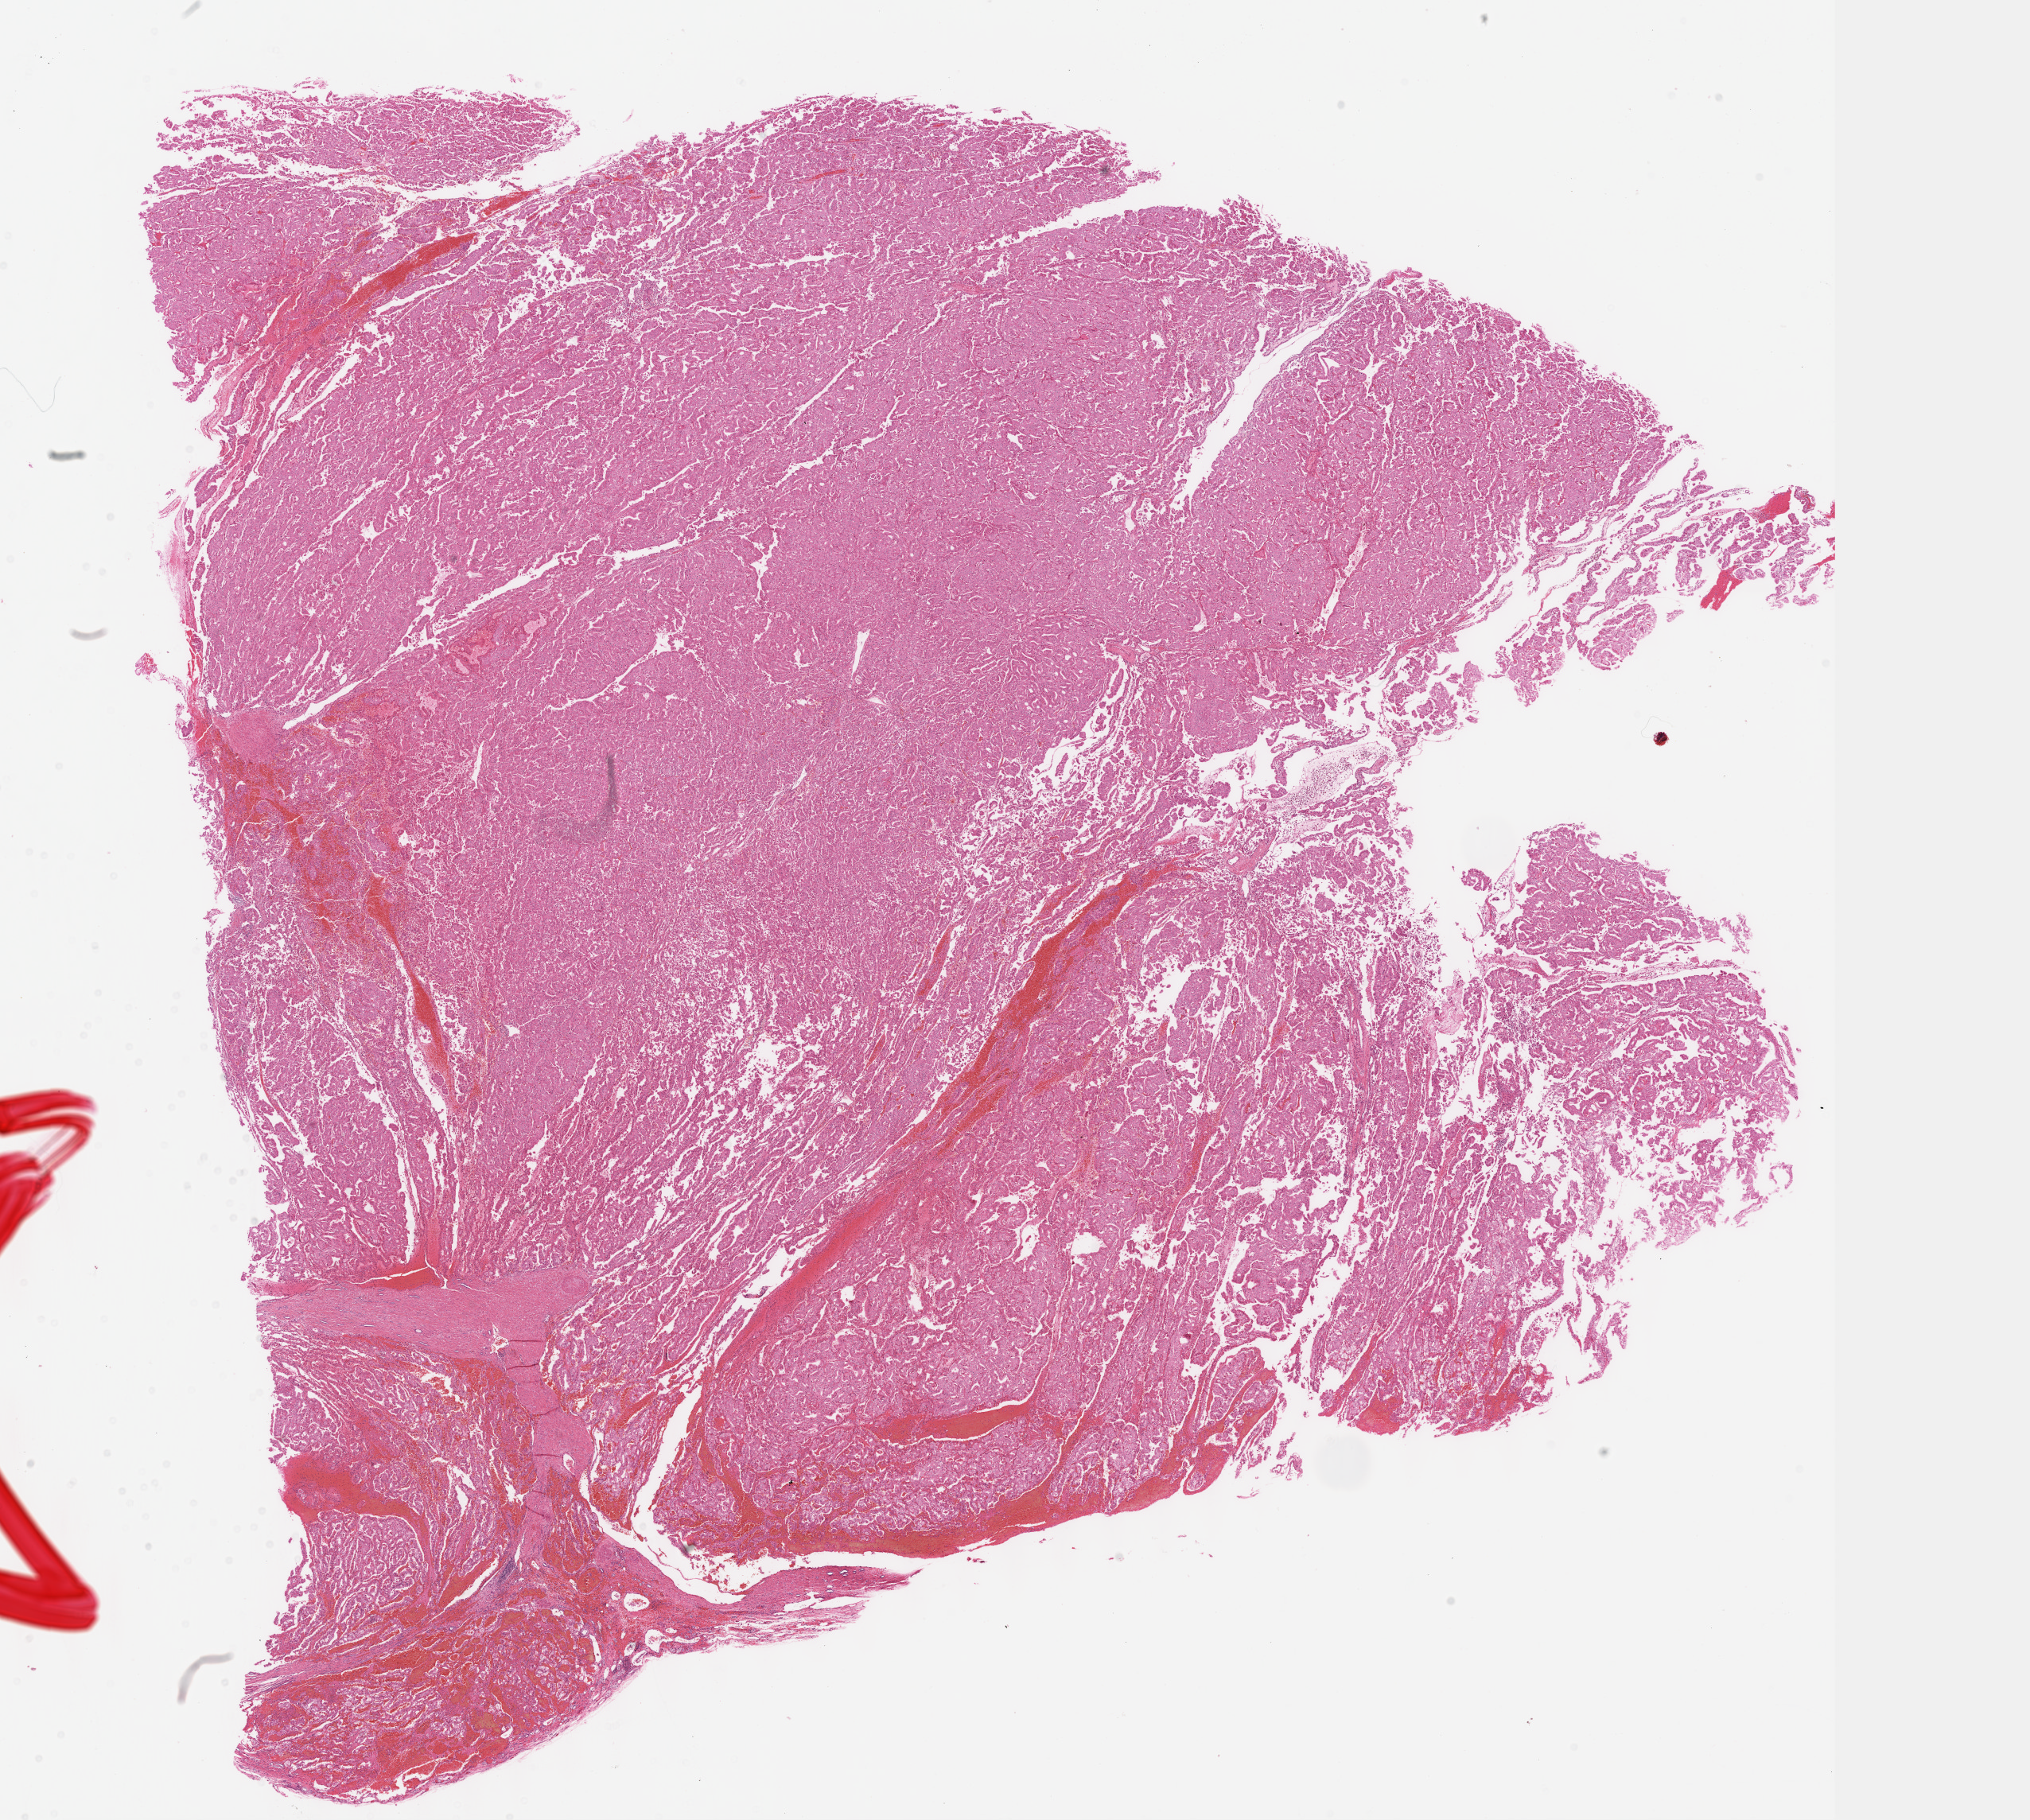
Whole-slide histology image, H&E, shown as a low-resolution overview of the whole scanned area (about 20.6 x 18.5 mm). Formalin-fixed paraffin-embedded (FFPE) diagnostic section. Kidney, primary tumour sample. Female, age 50 years at initial diagnosis. Slide review estimates, as recorded: tumour cells 80%, tumour nuclei 92%, normal cells 0%, stromal cells 20%, necrosis 0%. Infiltration values recorded for this section: lymphocyte infiltration 3%, monocyte infiltration 3%, neutrophil infiltration 1%.
* pathologic diagnosis: Renal cell carcinoma, chromophobe type
* AJCC pathologic stage: I (6th edition)